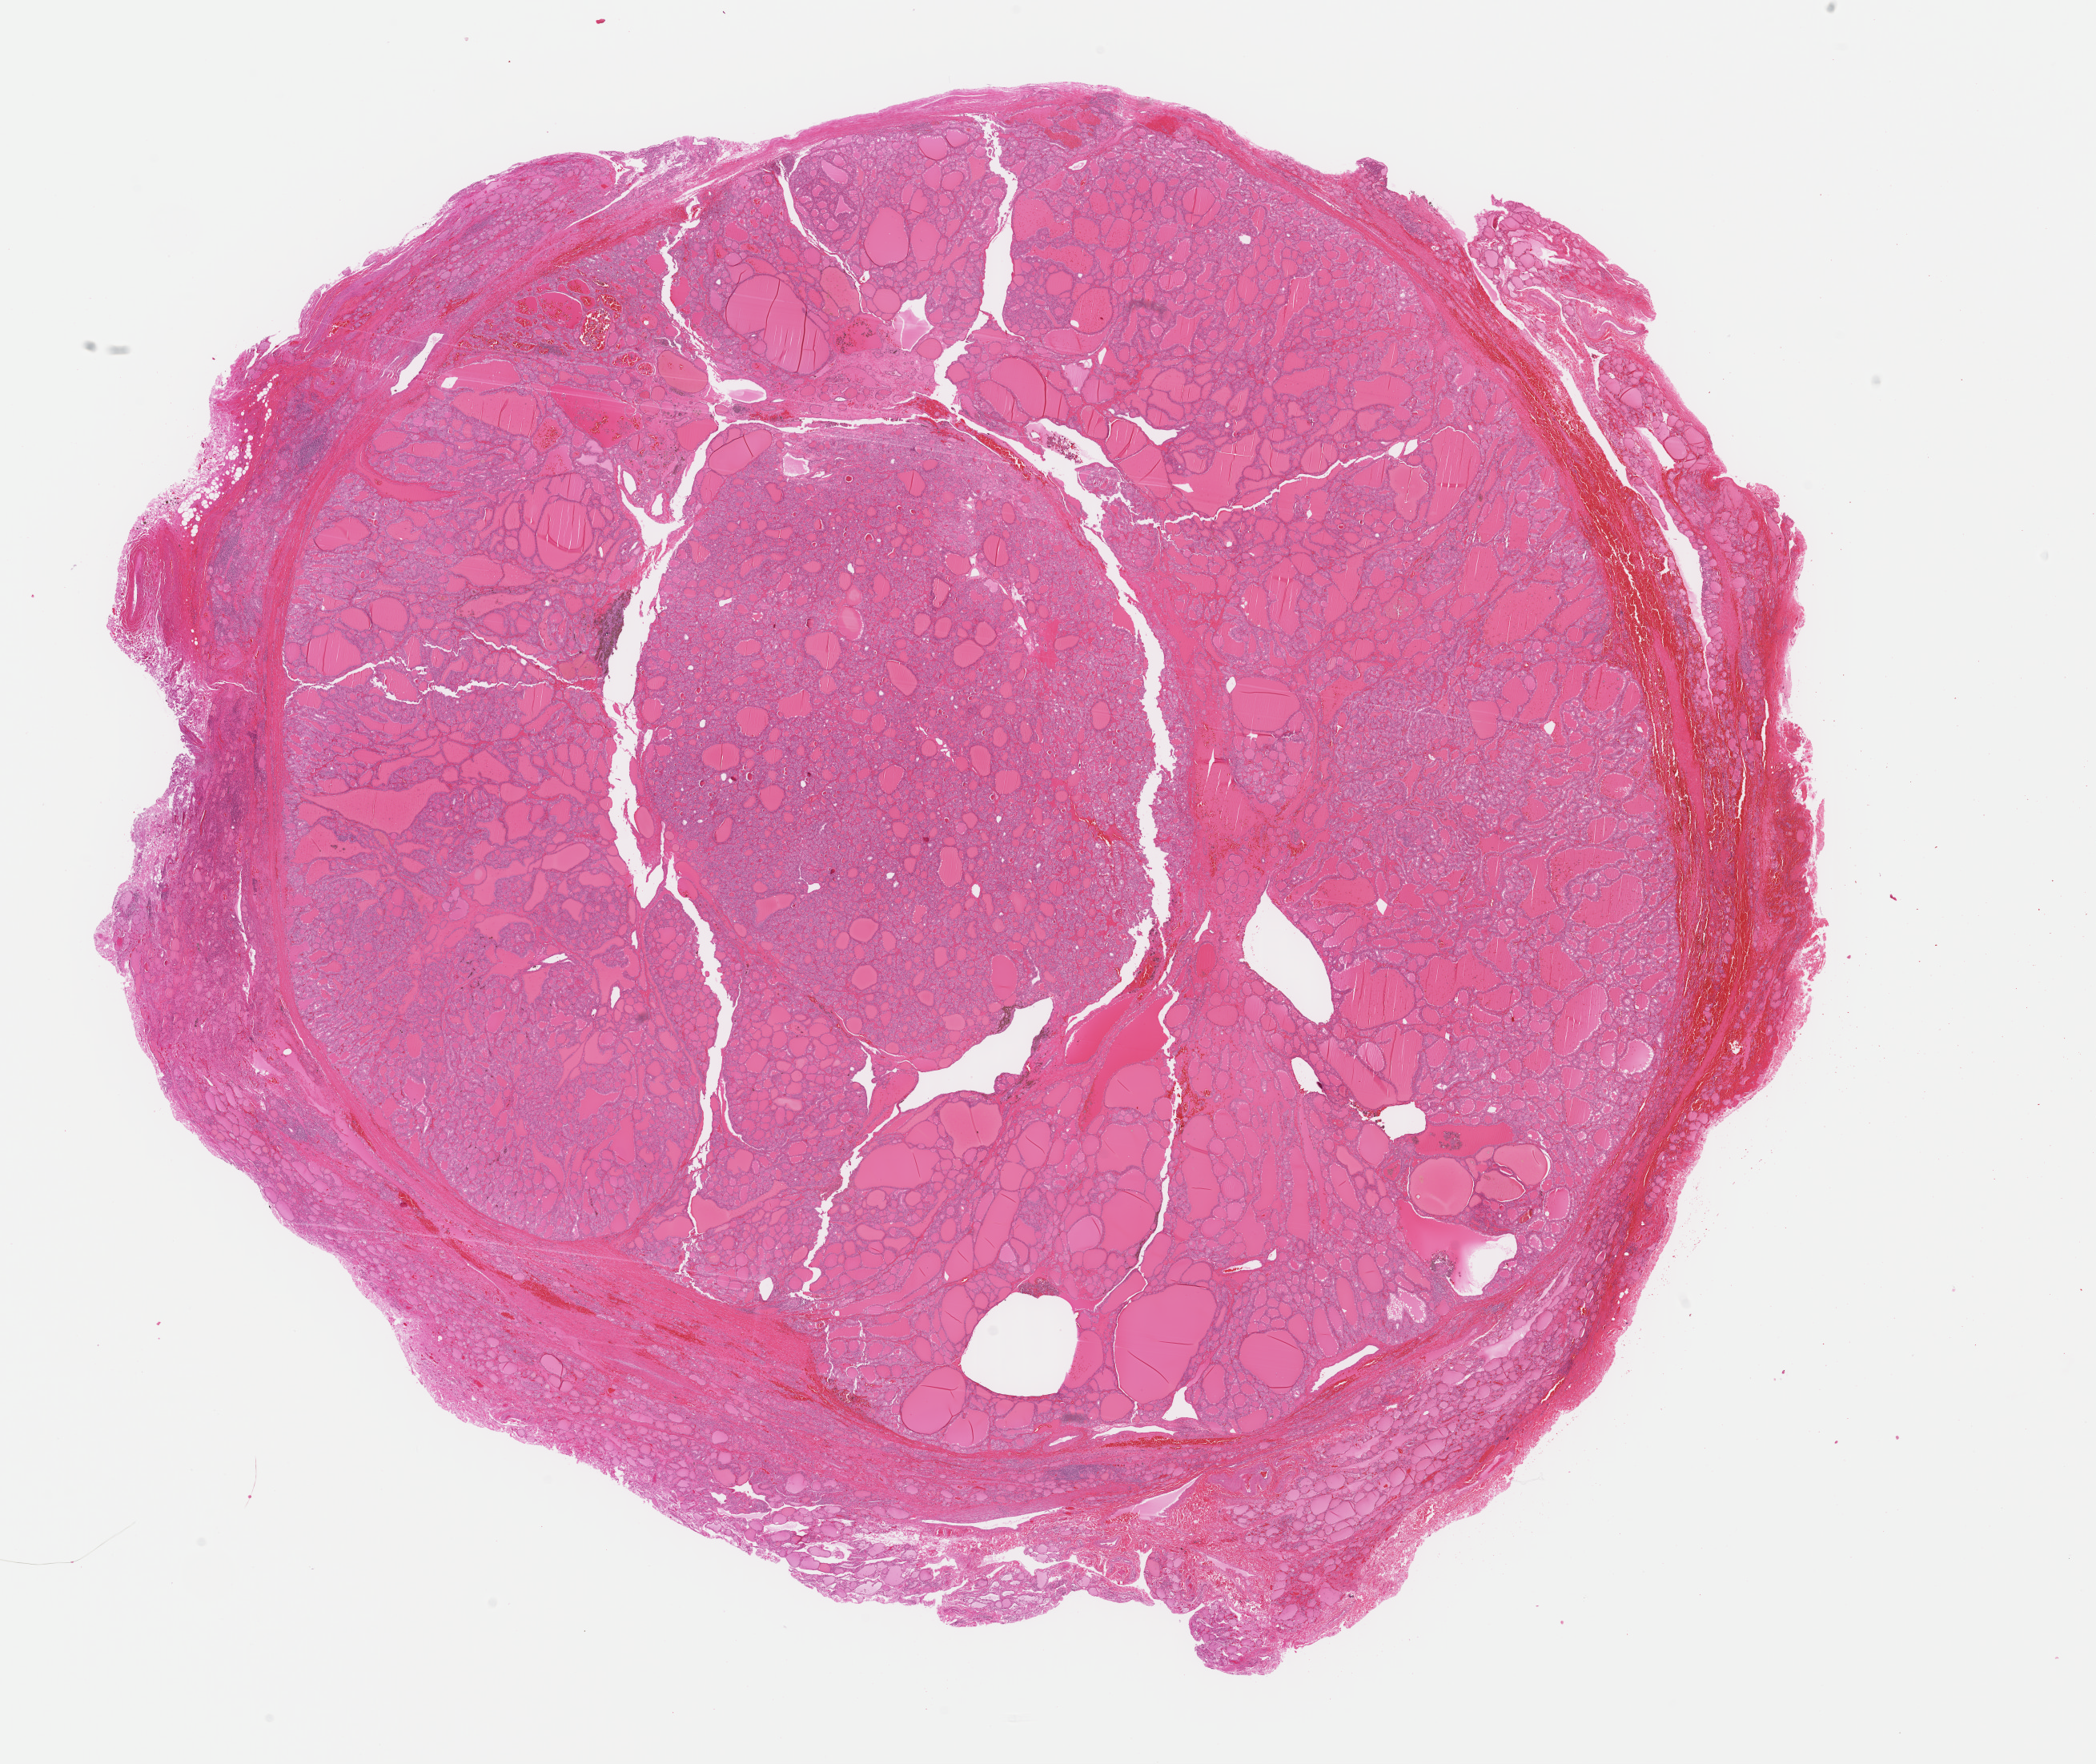
Digitized H&E-stained tissue section (whole slide) — shown as a low-resolution overview of the whole scanned area (about 20.7 x 17.4 mm, slide scanned at 40x), formalin-fixed paraffin-embedded (FFPE) diagnostic section, thyroid, primary tumour sample. Female patient; age at initial diagnosis 43 years.
Pathologic diagnosis: Papillary adenocarcinoma, NOS (thyroid gland). AJCC pathologic stage: I. Lymph nodes positive (case pathology): 0 of 1 examined.